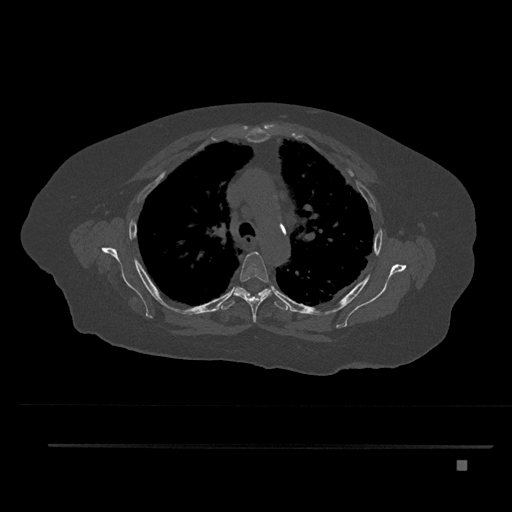
CT including the spine, one axial slice; position 592 of 797 along the scan axis; 120 kVp; bone window (W 1800 / L 400 HU); 0.5 mm slice thickness; 512 × 512 image matrix, field of view 437 × 437 mm. Female patient, age 76 years. From the clinical record (not read from this slice): primary cancer: lung; vertebrae with lytic lesions (as recorded): T11, L3.
Annotated regions visible in this slice (semi-automatically segmented with operator editing):
- T4 vertebra: bounding box [x1, y1, x2, y2] px = [234, 252, 272, 322]
- T5 vertebra: [219, 287, 289, 311]